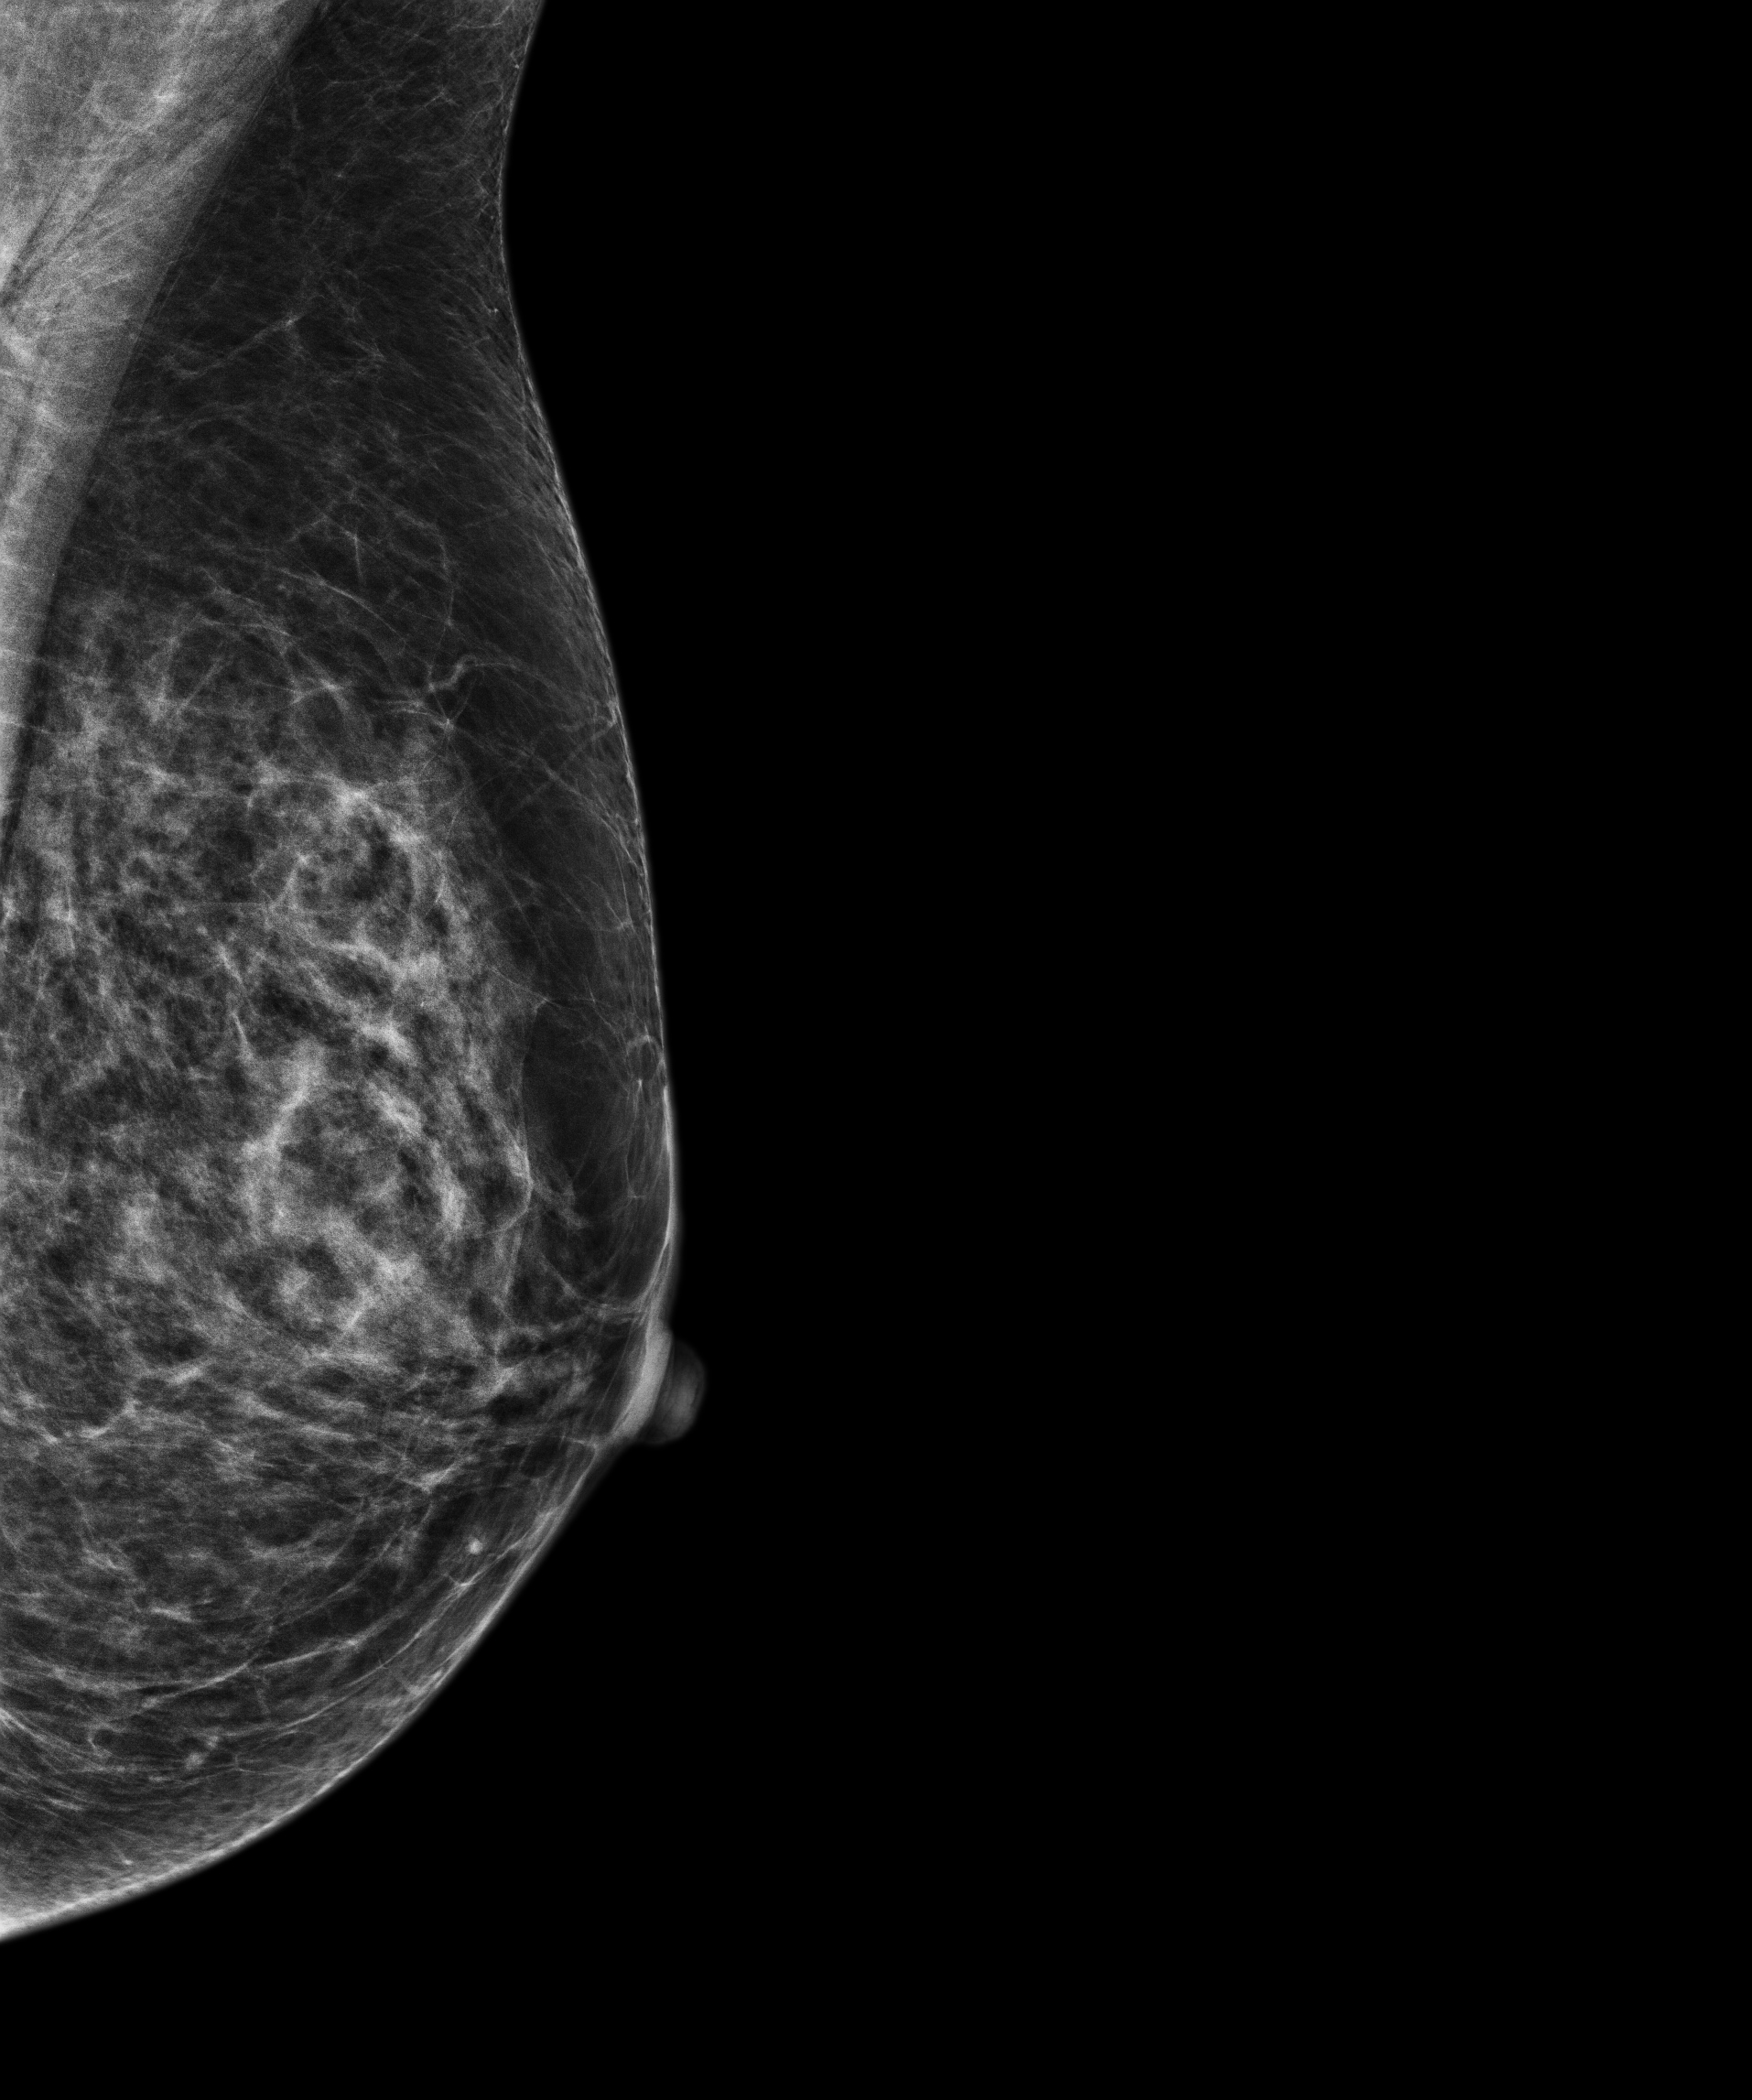
Screening examination. Patient aged 62 years (female).
Image type: full-field digital mammogram. Breast: left. Projection: MLO view.